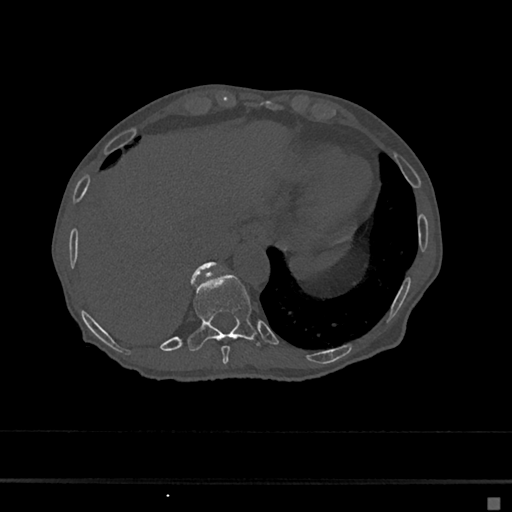
CT including the spine, one axial slice. Position 231 of 797 along the scan axis. 120 kVp. Bone window (W 1800 / L 400 HU). 0.5 mm slice thickness. 512 × 512 image matrix. Female patient, age 68 years. From the clinical record (not read from this slice): primary cancer: renal.
Annotated regions visible in this slice (semi-automatic segmentation, software-assisted and operator-edited):
- T10 vertebra: bounding box (x1, y1, x2, y2) in pixels: (188, 274, 256, 351)
- T11 vertebra: (192, 261, 218, 279)
- T9 vertebra: (221, 346, 231, 365)